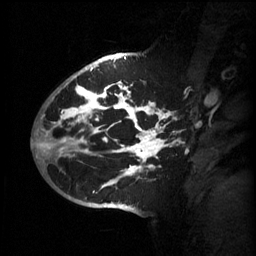
Breast MRI (dynamic contrast-enhanced), one sagittal slice; slice 40 of 60 in the series (ordered by position); 3 images stored at this slice position (order not interpretable as contrast timing); 1.5 T; TE 4.2 ms, TR 11 ms; 2 mm slice thickness; 256 × 256 image matrix. Female patient, age 51 years.
Outlined on this slice (semi-automatic segmentation, software-assisted and operator-edited):
- analysis volume of interest (the breast-tissue region the enhancement analysis was run in; not a lesion): bounding box <63,80,182,201> (left, top, right, bottom; pixels)
- tumour enhancement mask (voxels above the 70 % enhancement threshold inside the analysis volume of interest): <63,82,181,187>